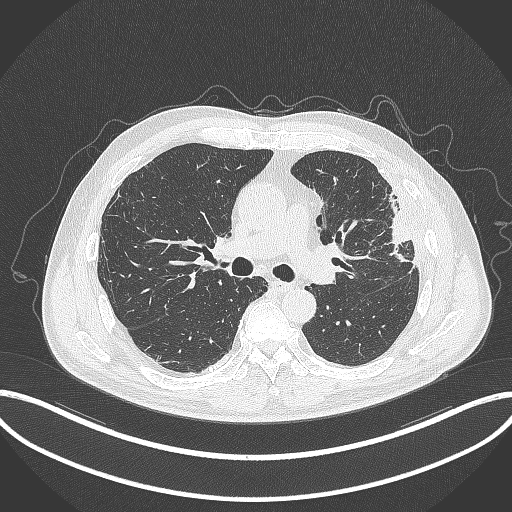
Chest CT, one axial slice. Position 205 of 382 along the scan axis. Reconstruction kernel B70f. Lung window (W 1500 / L -600 HU). 512 × 512 image matrix. Male patient, age 64 years. Case-level facts recorded for this patient, not image findings: clinical TNM (as recorded): T4 N1 M0; histopathological grade: G3.
Structures marked on this image (rectangle marked by the reading radiologist):
- lung tumour (recorded histology: adenocarcinoma): box from (x=379, y=190) to (x=416, y=270) px